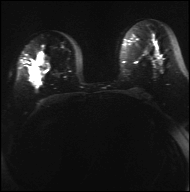
Breast MRI, one axial slice; slice 19 of 42 in the series (ordered by position); diffusion-weighted series; image 2 of 4 stored at this slice position (different b-values; order by instance number); 3 T; 4 mm slice thickness; 190 × 192 image matrix, field of view 317 × 320 mm. Female patient.
Outlined on this slice (expert manual segmentation):
- tumour on diffusion-weighted imaging: bounding box [x1, y1, x2, y2] px = [75, 64, 99, 75]